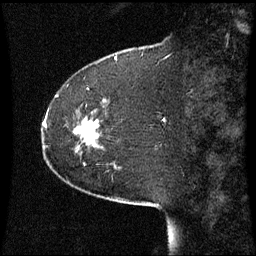
Breast MRI (dynamic contrast-enhanced), one sagittal slice. Dynamic contrast-enhanced series, image 2 of 3 at this slice position (ordered by acquisition). 1.5 T. TE 4.2 ms, TR 8.9 ms. 2.2 mm slice thickness. 256 × 256 image matrix, field of view 220 × 220 mm. Patient: female, 51 years. Case-level facts recorded for this patient, not image findings: setting: breast cancer imaged before/during neoadjuvant chemotherapy; receptor status: HR-positive, HER2-negative.
Annotated regions visible in this slice (semi-automatically segmented with operator editing):
- analysis volume of interest (the breast-tissue region the enhancement analysis was run in; not a lesion): bounding box [x1, y1, x2, y2] px = [44, 118, 103, 165]
- tumour enhancement mask (voxels above the 70 % enhancement threshold inside the analysis volume of interest): [76, 120, 99, 143]